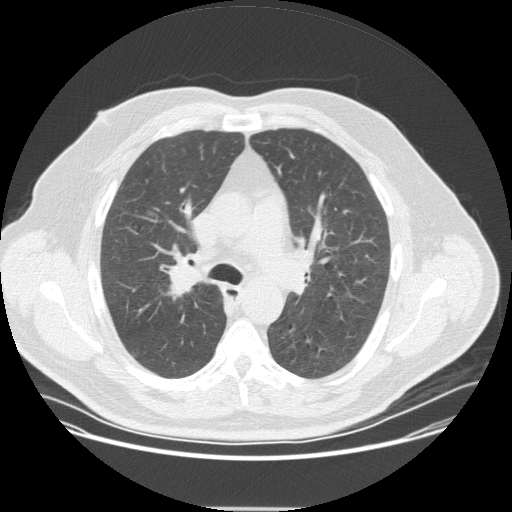
Low-dose screening chest CT, one axial slice. Position 229 of 351 along the scan axis. Reconstruction kernel STANDARD. Lung window (W 1500 / L -600 HU). 2.5 mm slice thickness. 512 × 512 image matrix.
Outlined on this slice (outlined manually by an expert reader):
- lesion 1 (tumor, upper lobe of right lung): bounding box <166,269,203,302> (left, top, right, bottom; pixels)